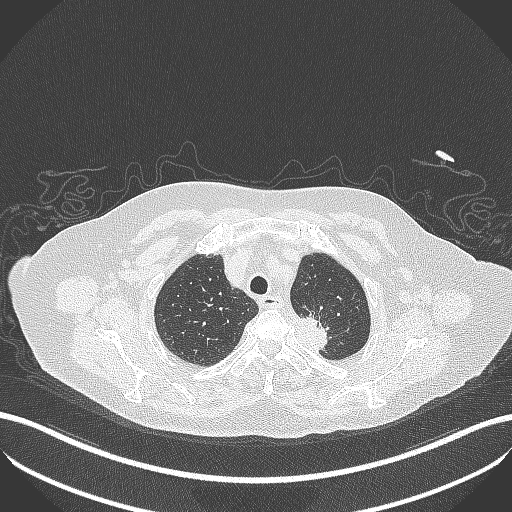
Chest CT, one axial slice; slice 287 of 353 in the series (ordered by position); 100 kVp; lung window (W 1500 / L -600 HU); 512 × 512 image matrix. Patient: female, 81 years. Case-level facts recorded for this patient, not image findings: clinical TNM (as recorded): T2a N0 M0.
Annotated regions visible in this slice (bounding box drawn by a radiologist):
- lung tumour (recorded histology: adenocarcinoma): bounding box (x1, y1, x2, y2) in pixels: (292, 306, 342, 352)